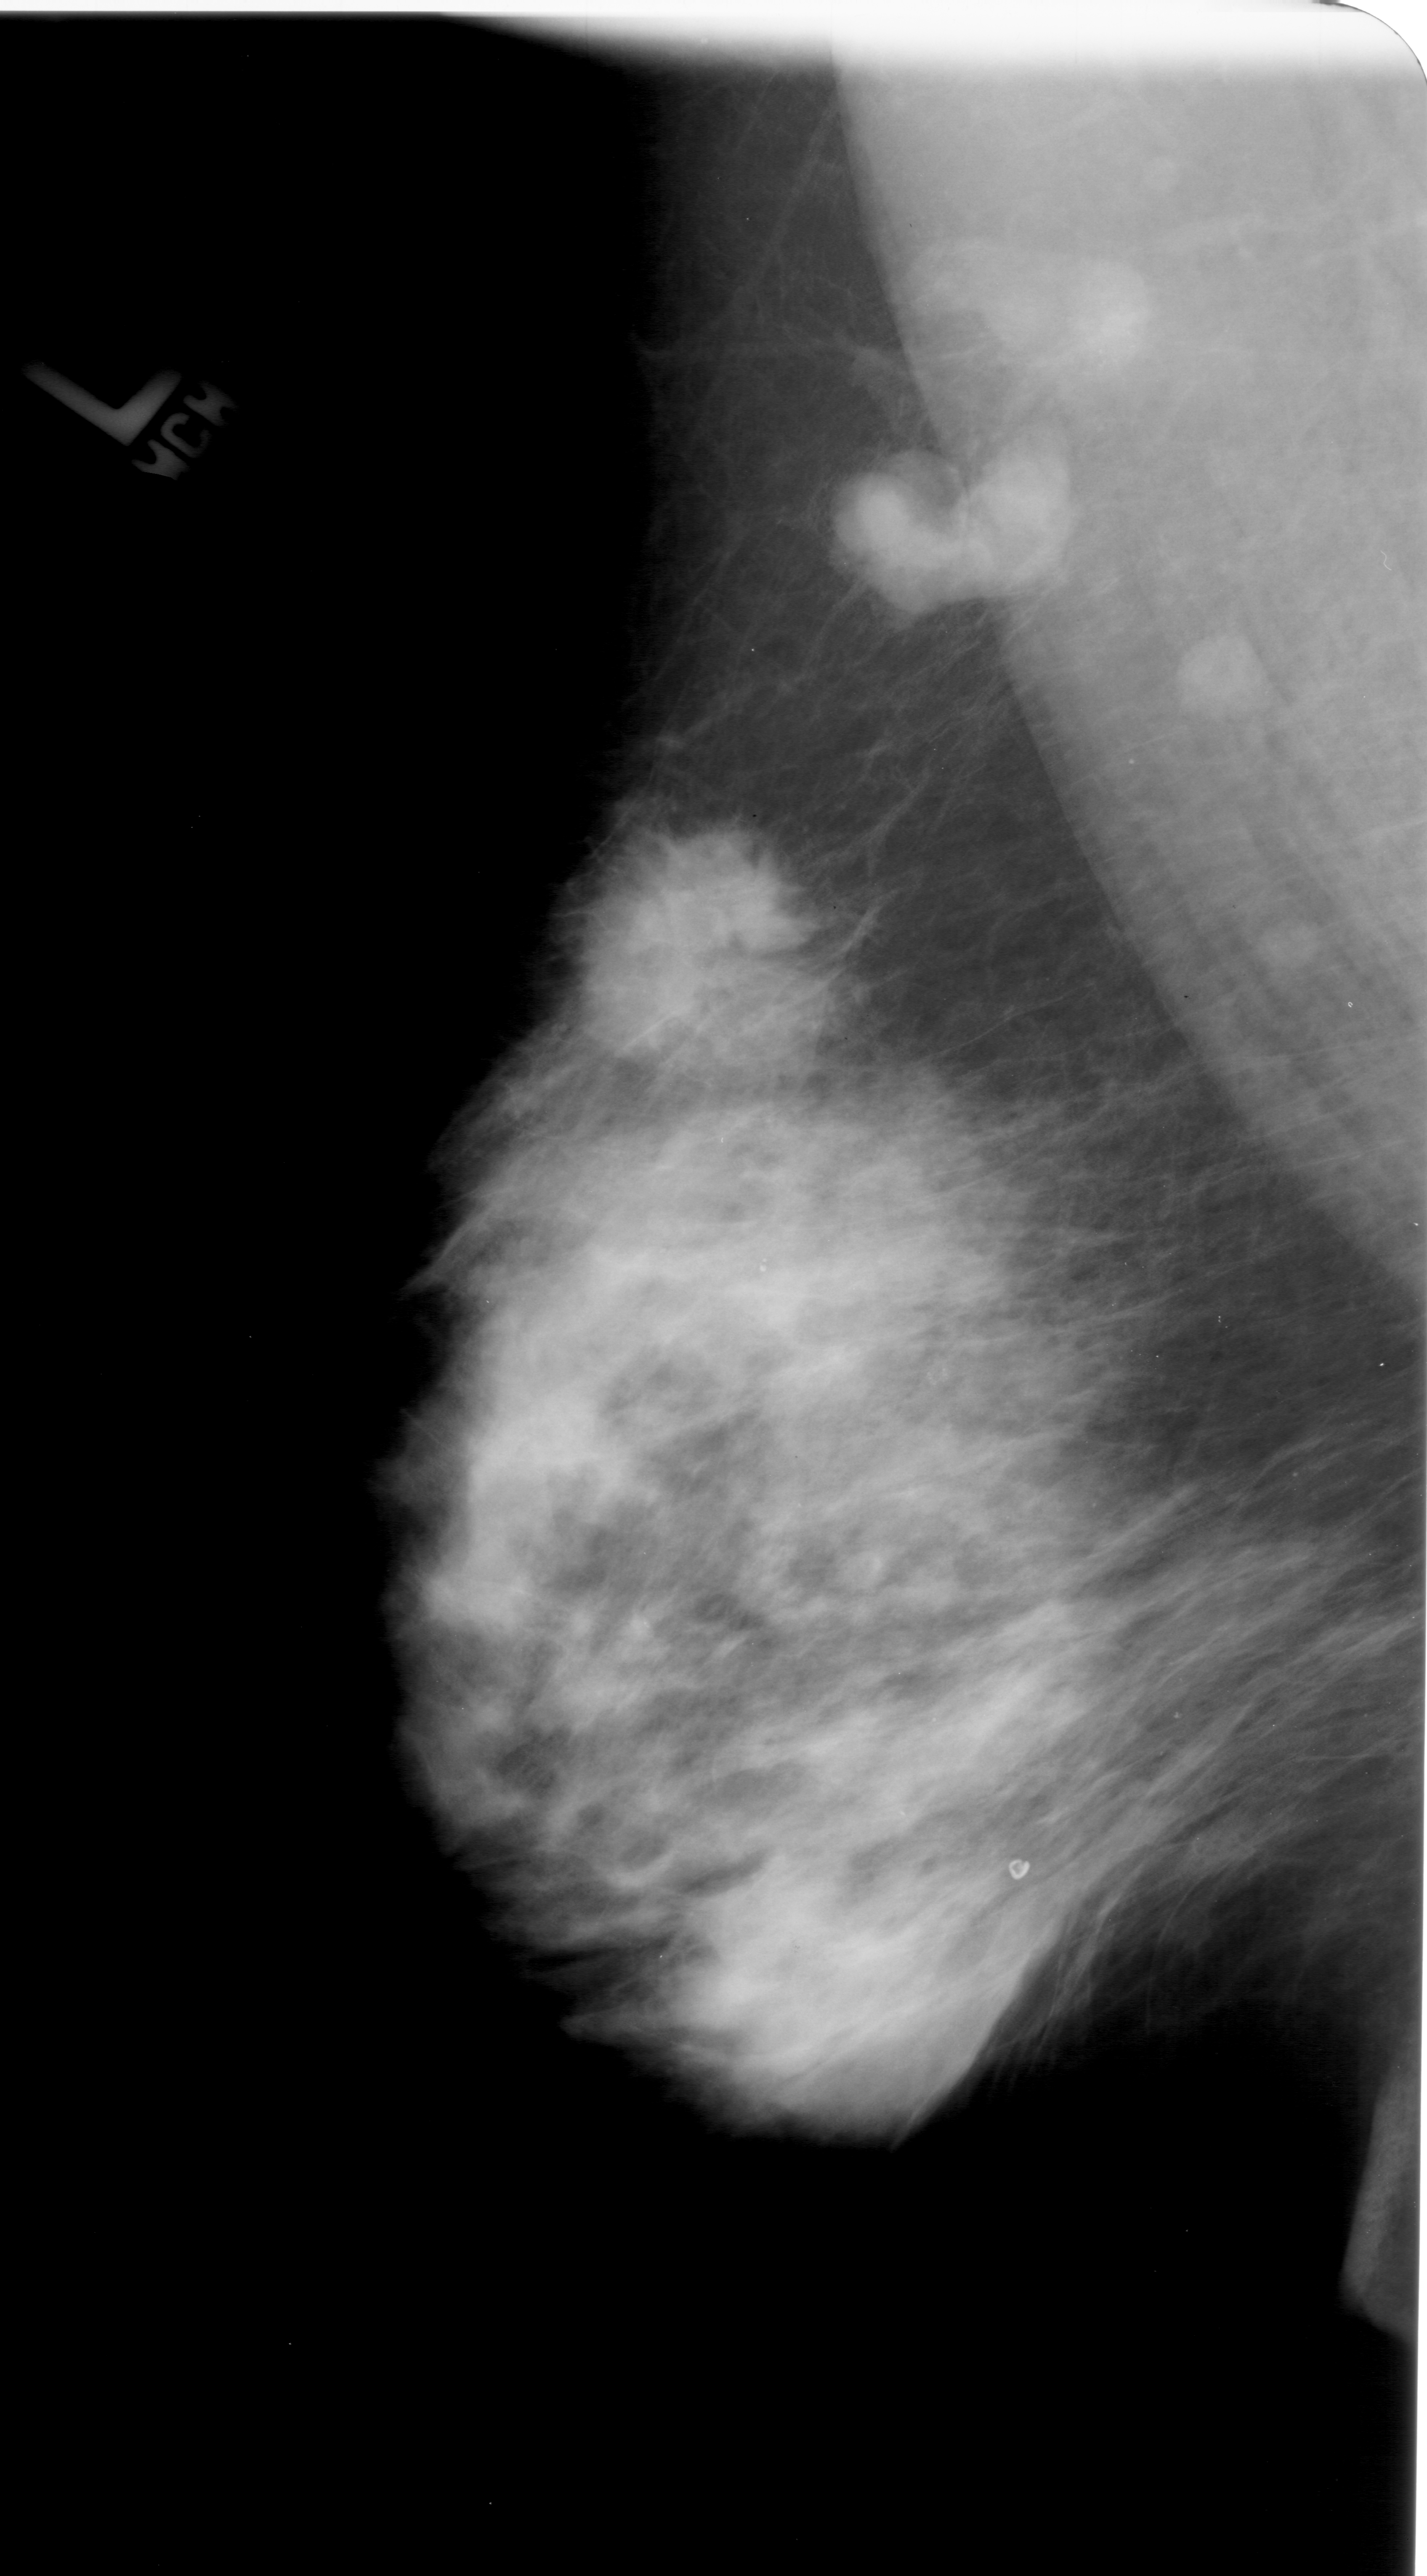
Digitized screen-film mammogram; left breast; MLO view.
Abnormality record for this image: mass, shape irregular, margins spiculated; BI-RADS assessment category 5; subtlety rating 5 on a 1 (subtle) to 5 (obvious) scale; pathology result (as recorded, not read from the image): malignant.